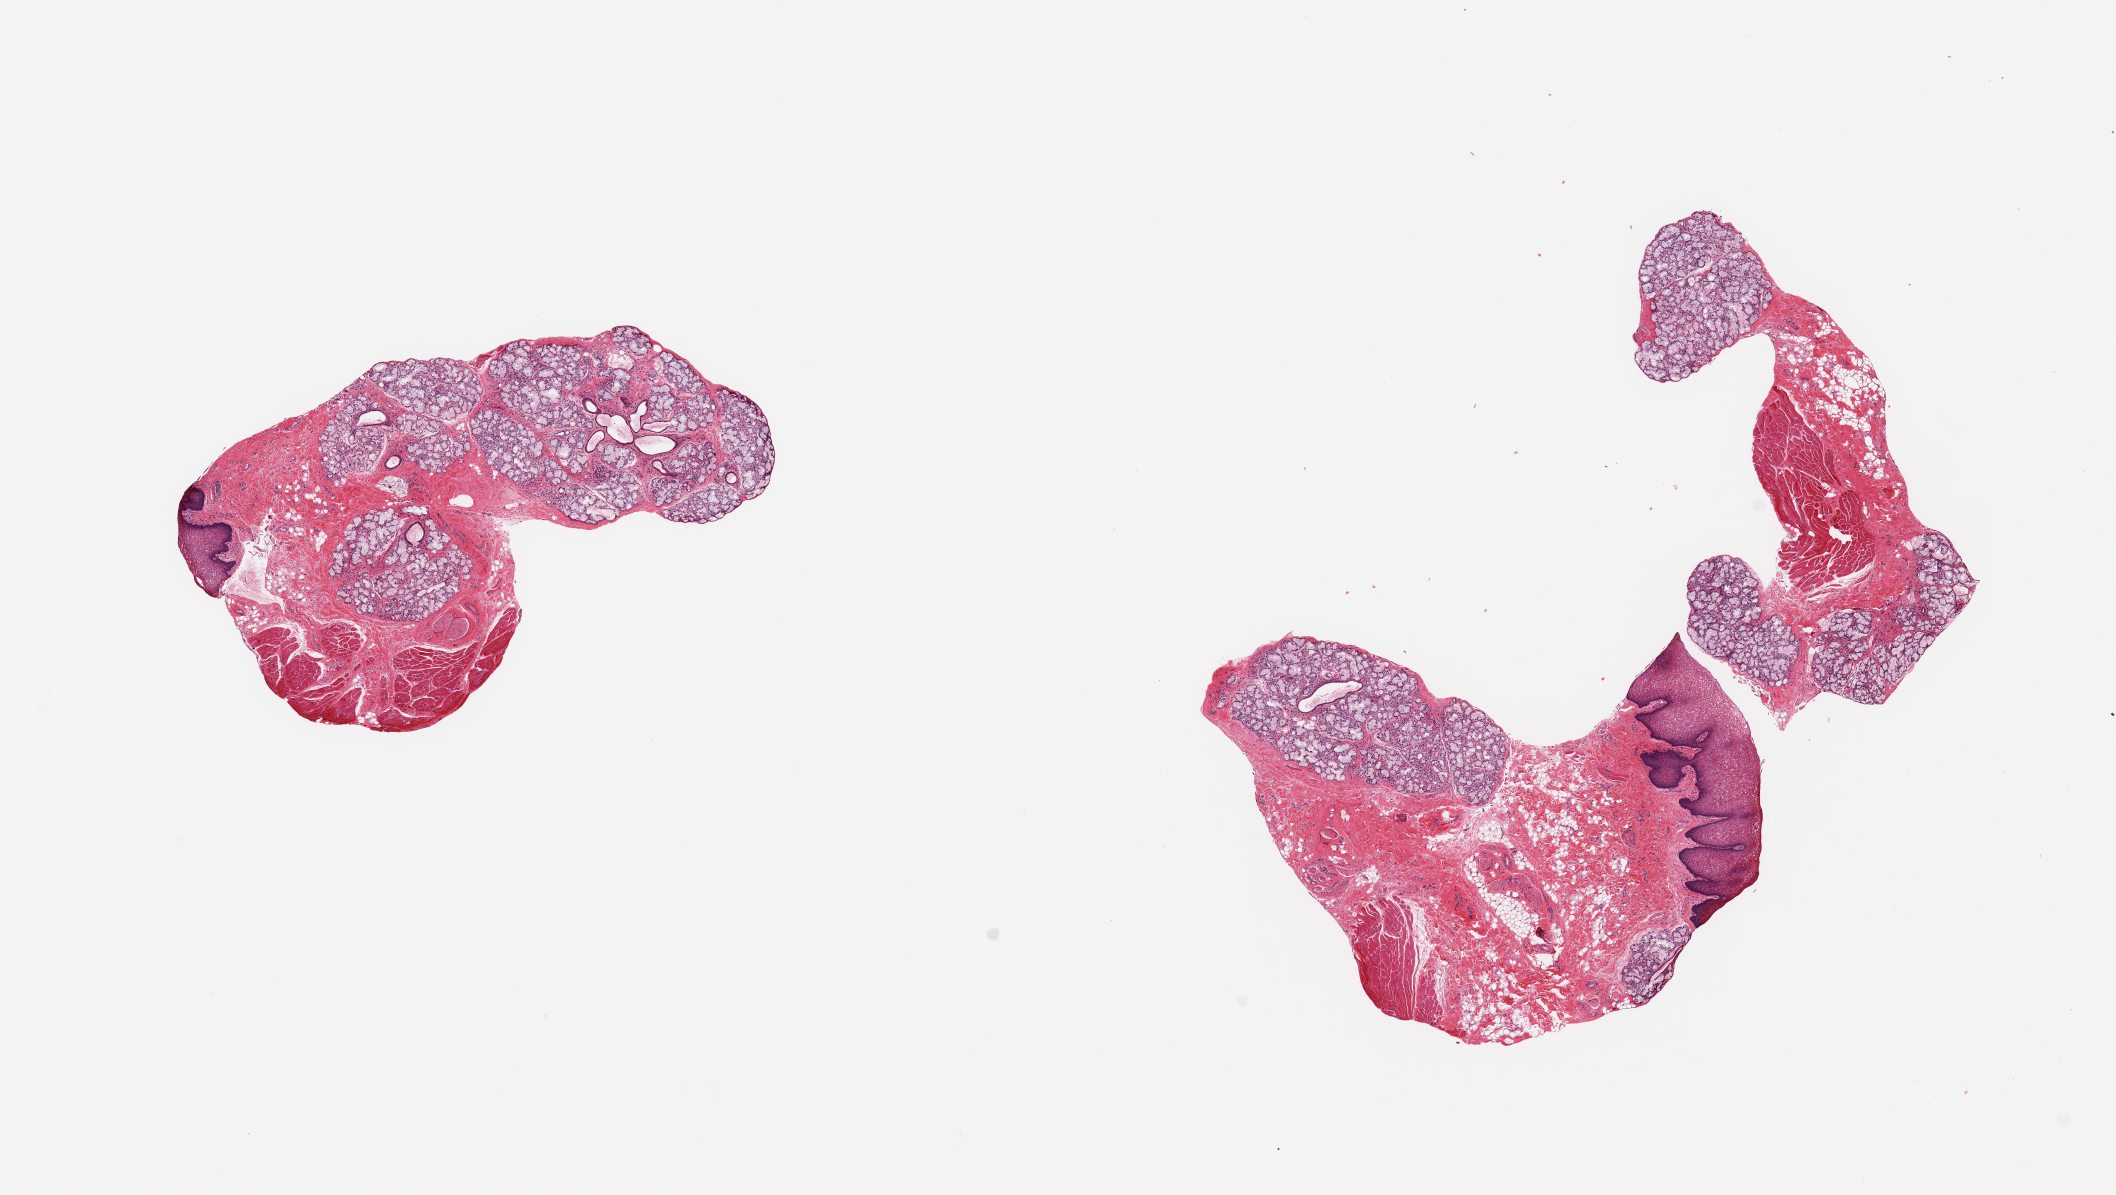
Whole-slide image, haematoxylin and eosin stain, brightfield — shown as a low-resolution overview of the whole scanned area (about 16.7 x 9.5 mm), PAXgene-fixed paraffin-embedded (PFPE) section, section of minor salivary gland (target tissue), donor tissue sample. Donor: male.
Pathologist's review note for this sample: 2 pieces; ~50% is salivary gland, remainder is lip/stroma/skeletal muscle/fat.